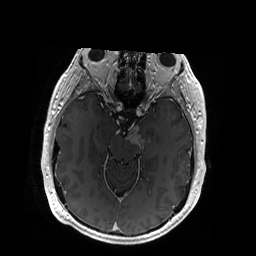
Brain MRI from a brain-tumour surgery series, one axial slice; slice 118 of 192 in the series (ordered by position); T1-weighted post-contrast; 256 × 256 image matrix. Case-level facts recorded for this patient, not image findings: histopathology: Glioblastoma; WHO grade: 4; IDH mutation: no.
Structures marked on this image (outlined manually by an expert reader):
- tumour: bounding box <126,126,142,145> (left, top, right, bottom; pixels)